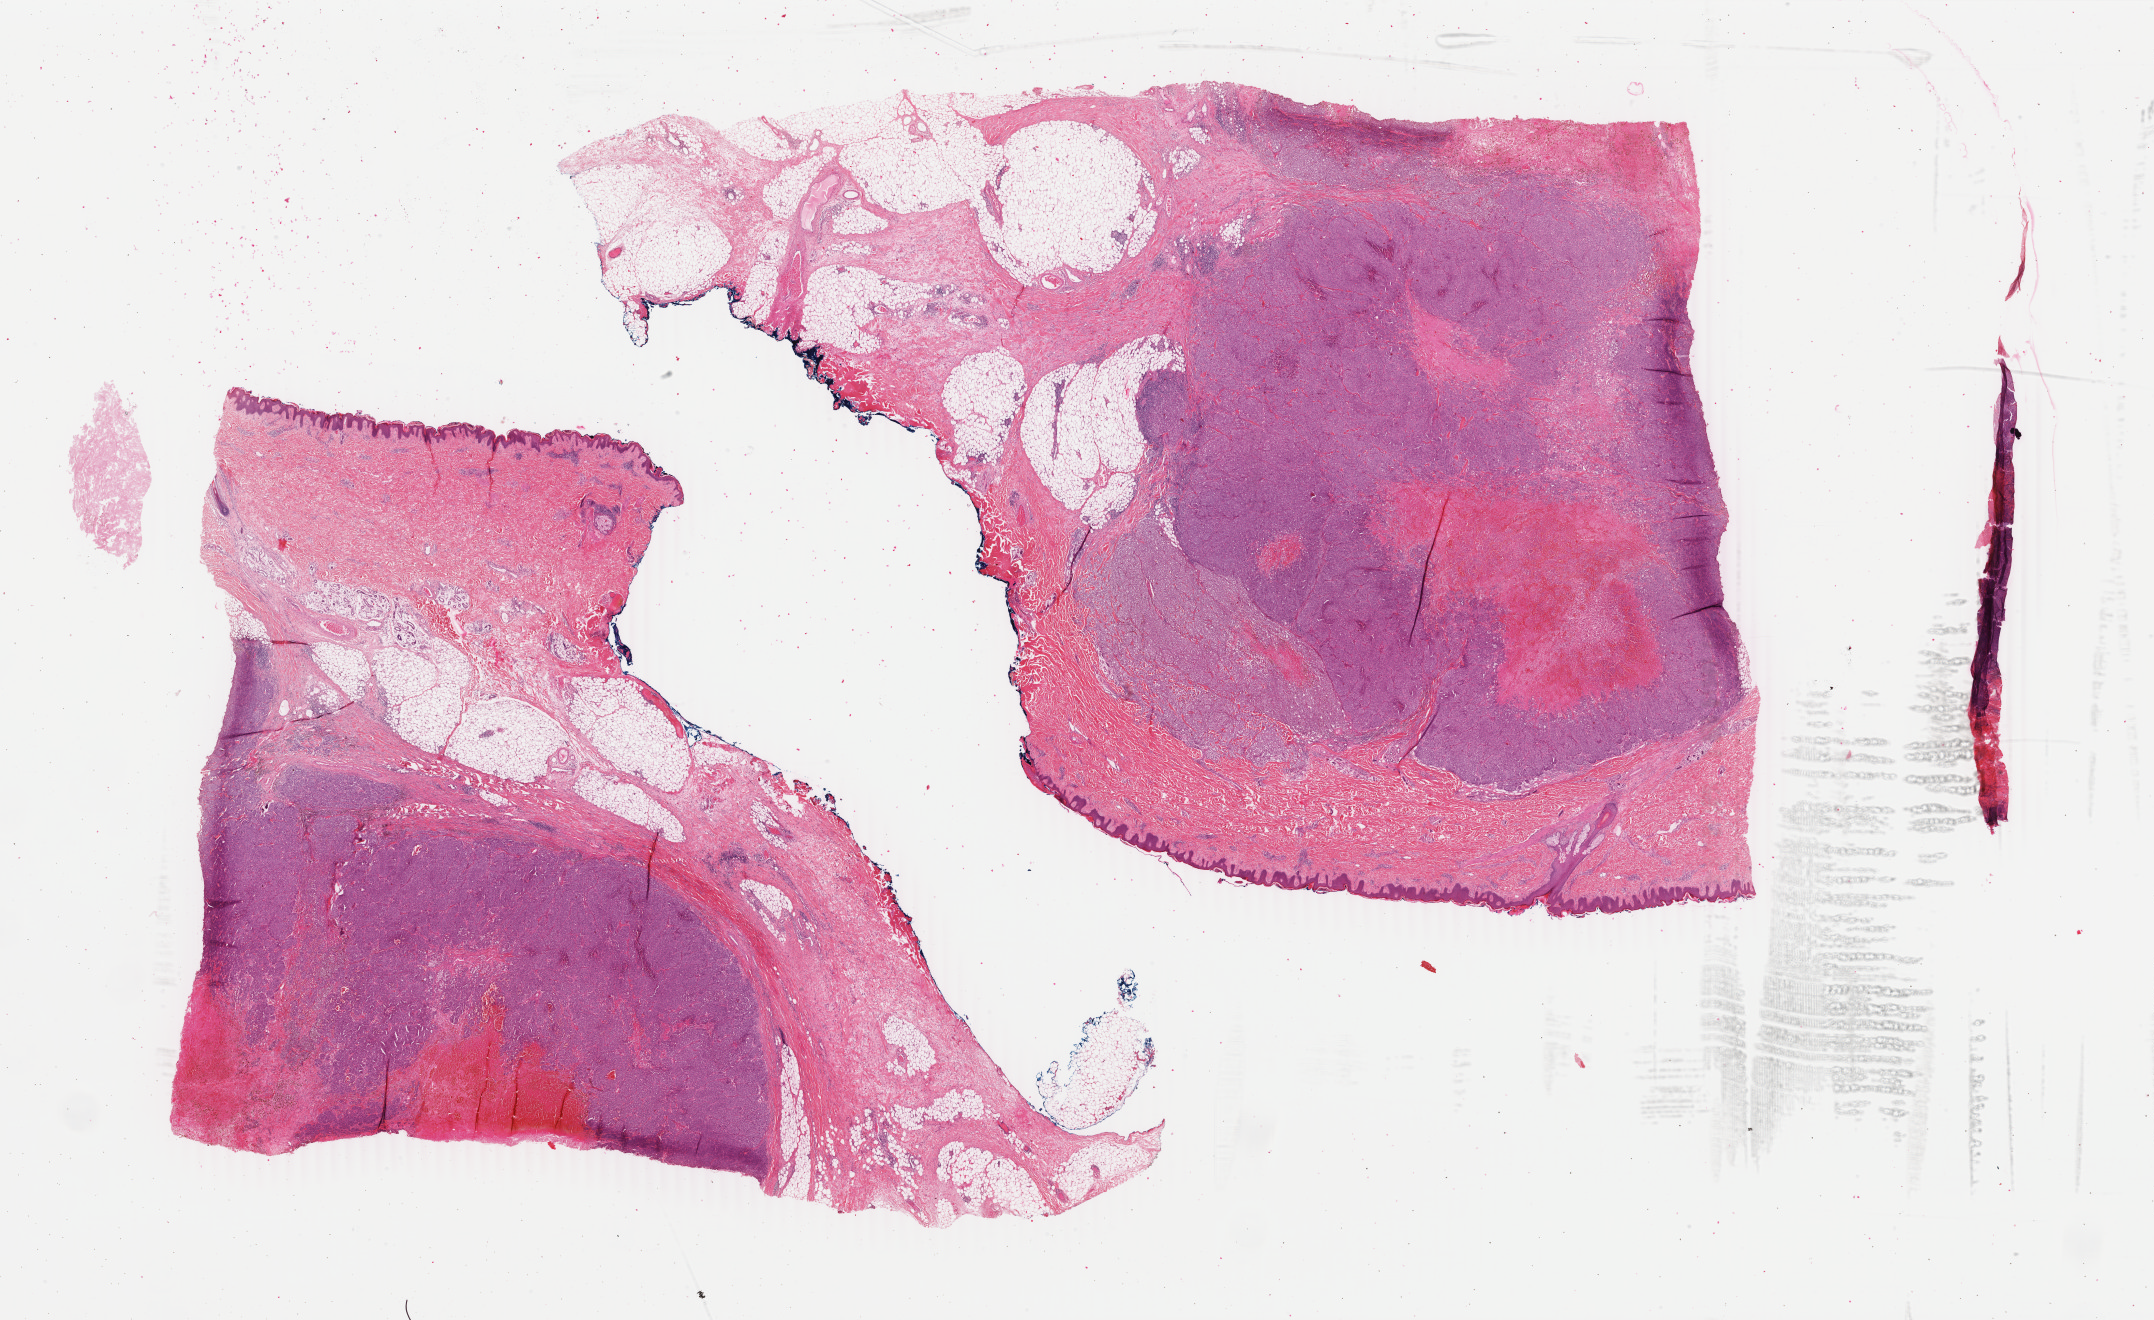
H&E-stained whole-slide image — low-resolution overview of the scanned area, about 34.3 x 21.0 mm (slide scanned at 40x). FFPE section. Sample: primary tumour, skin. Patient: male, age at initial diagnosis 20 years.
Histologic diagnosis: Malignant melanoma, NOS.